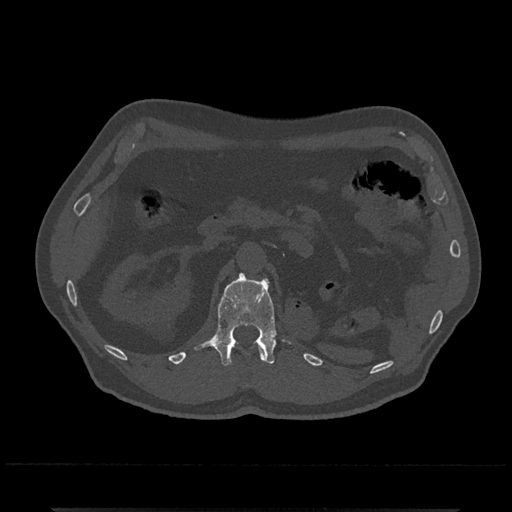
CT including the spine, one axial slice; slice 374 of 797 in the series (ordered by position); 120 kVp; bone window (W 1800 / L 400 HU); 0.5 mm slice thickness; 512 × 512 image matrix, field of view 393 × 393 mm. Patient: male, 67 years. Case-level facts recorded for this patient, not image findings: primary cancer: prostate.
Annotated regions visible in this slice (semi-automatic segmentation, software-assisted and operator-edited):
- L1 vertebra: bounding box (x1, y1, x2, y2) in pixels: (193, 272, 298, 366)
- T12 vertebra: (259, 346, 266, 361)